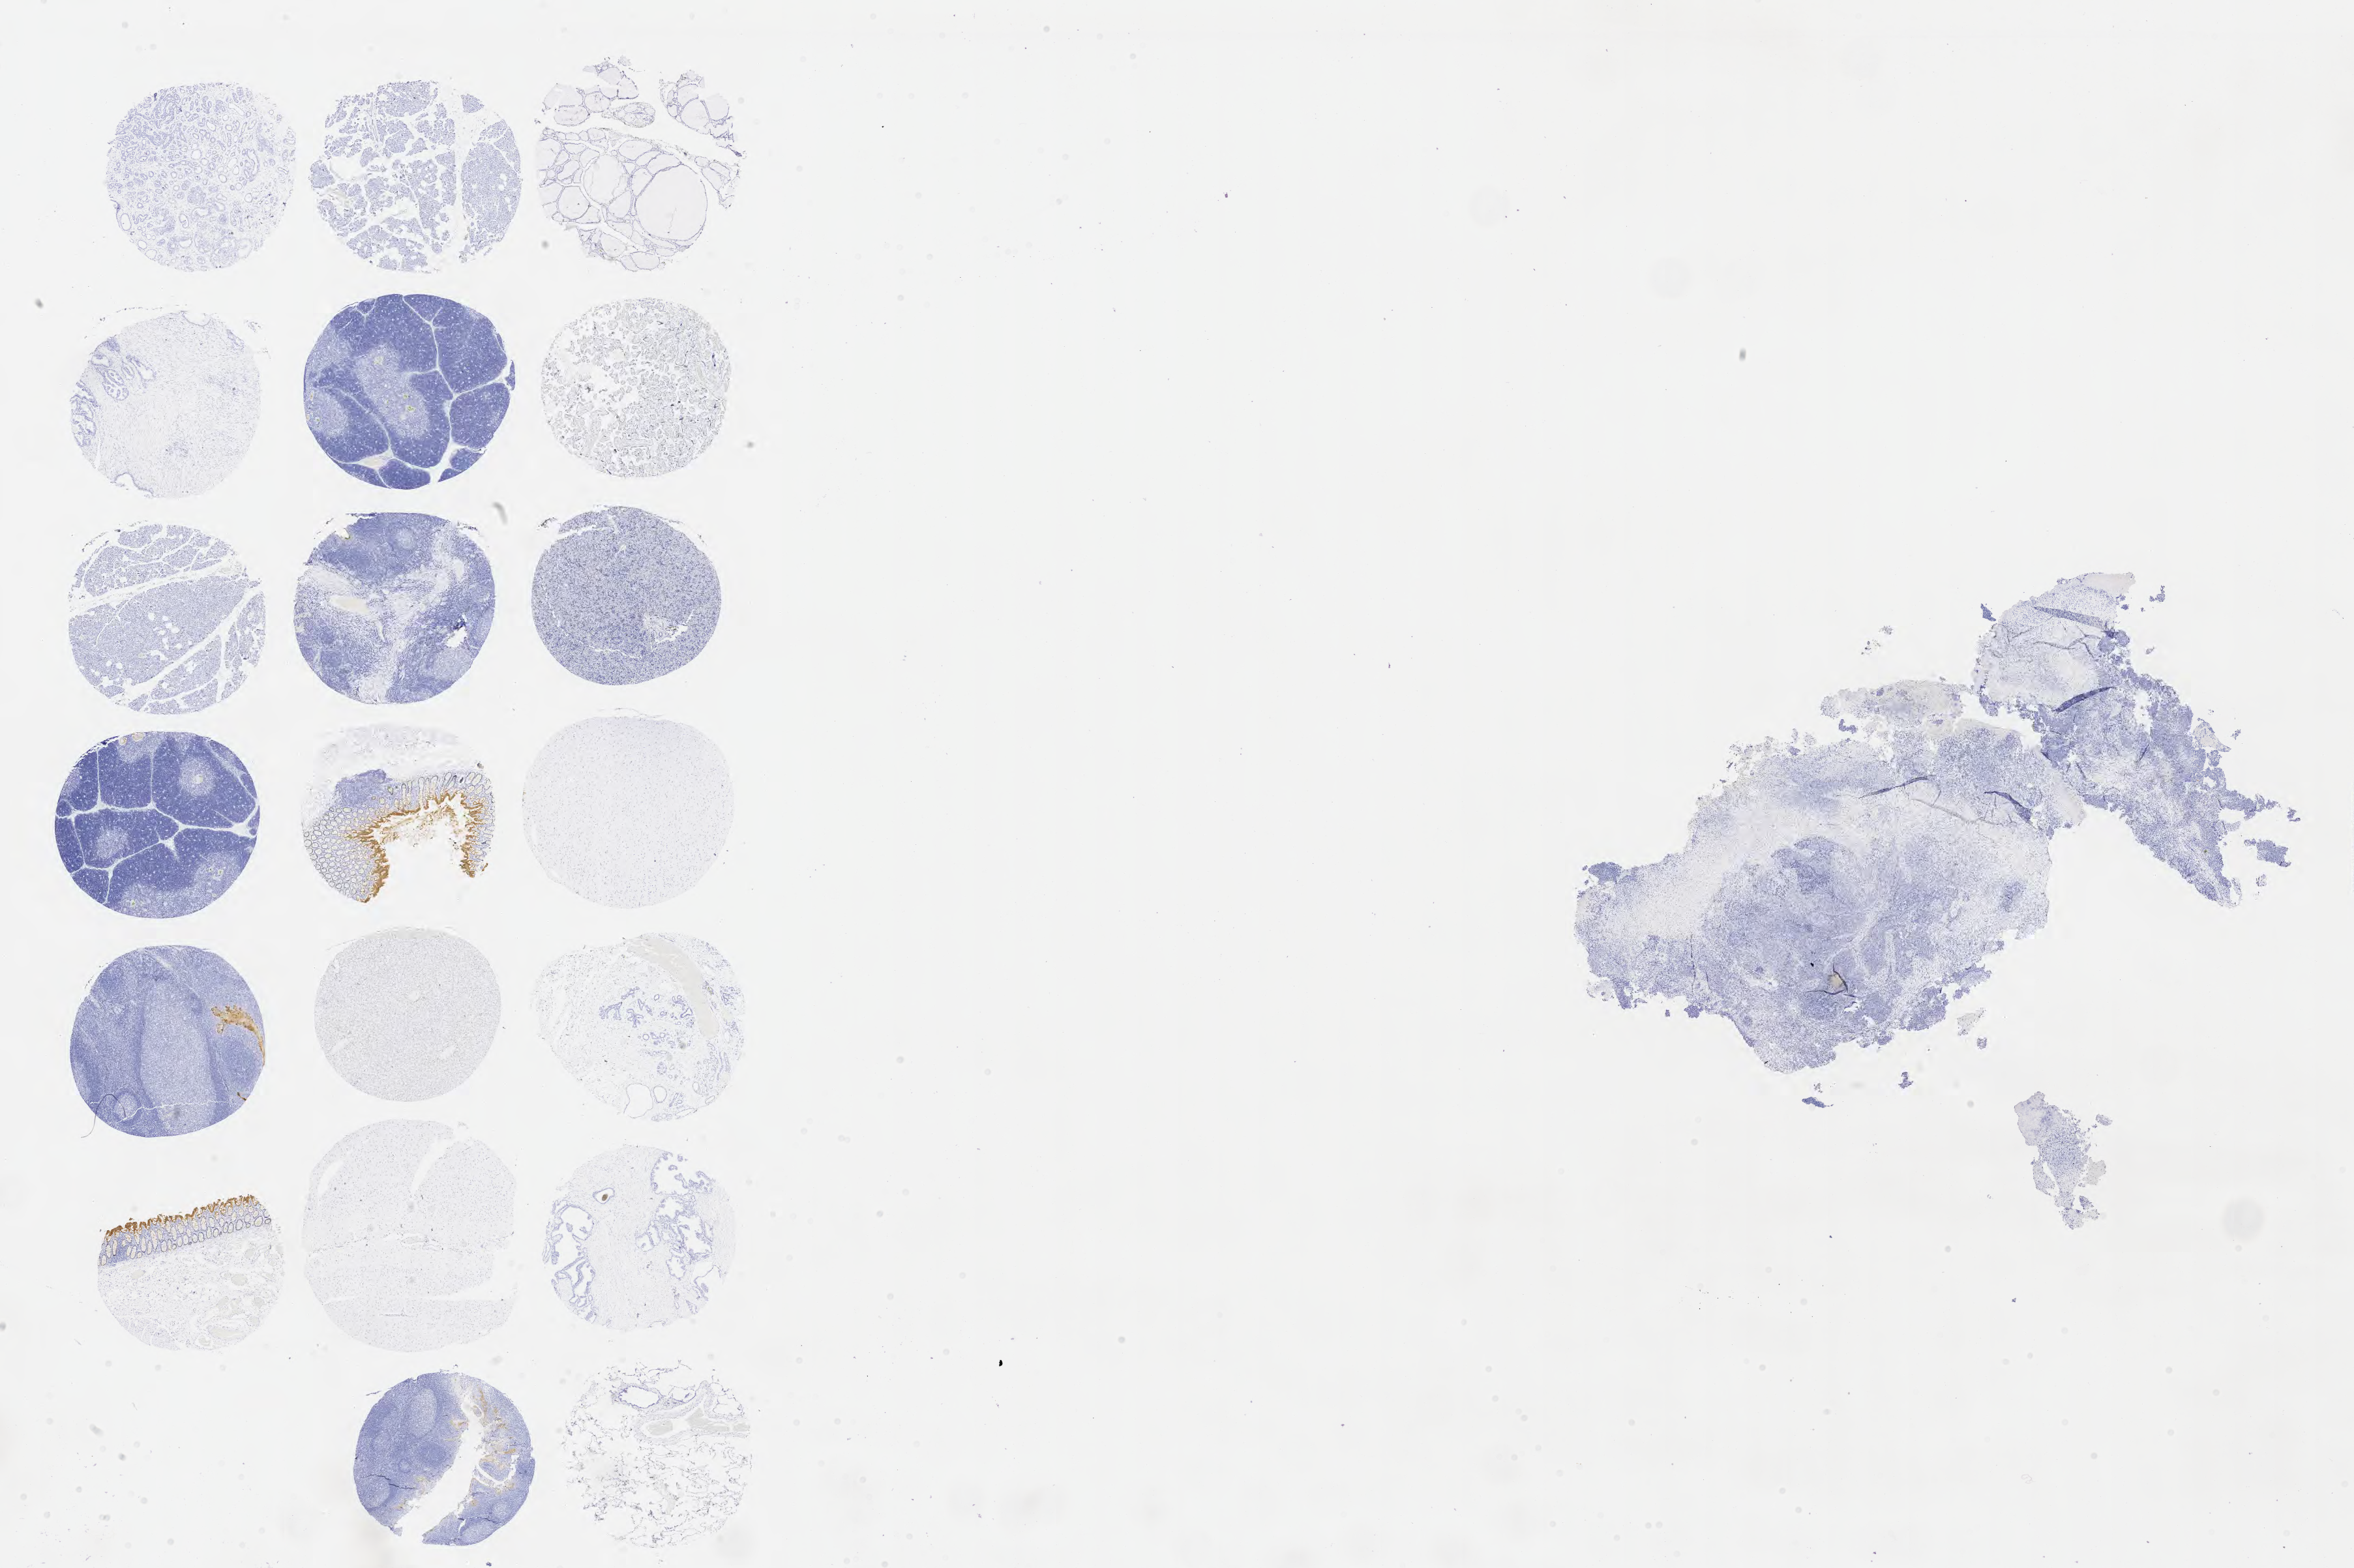
Immunohistochemistry (IHC) whole-slide image stained for carcinoembryonic antigen (CEA), shown as a low-resolution overview of the whole scanned area (about 29.2 x 19.4 mm); specimen: tumor tissue; site: cervix. Patient: female, aged 65.
Diagnosis: Squamous cell carcinoma, large cell, nonkeratinizing, NOS.